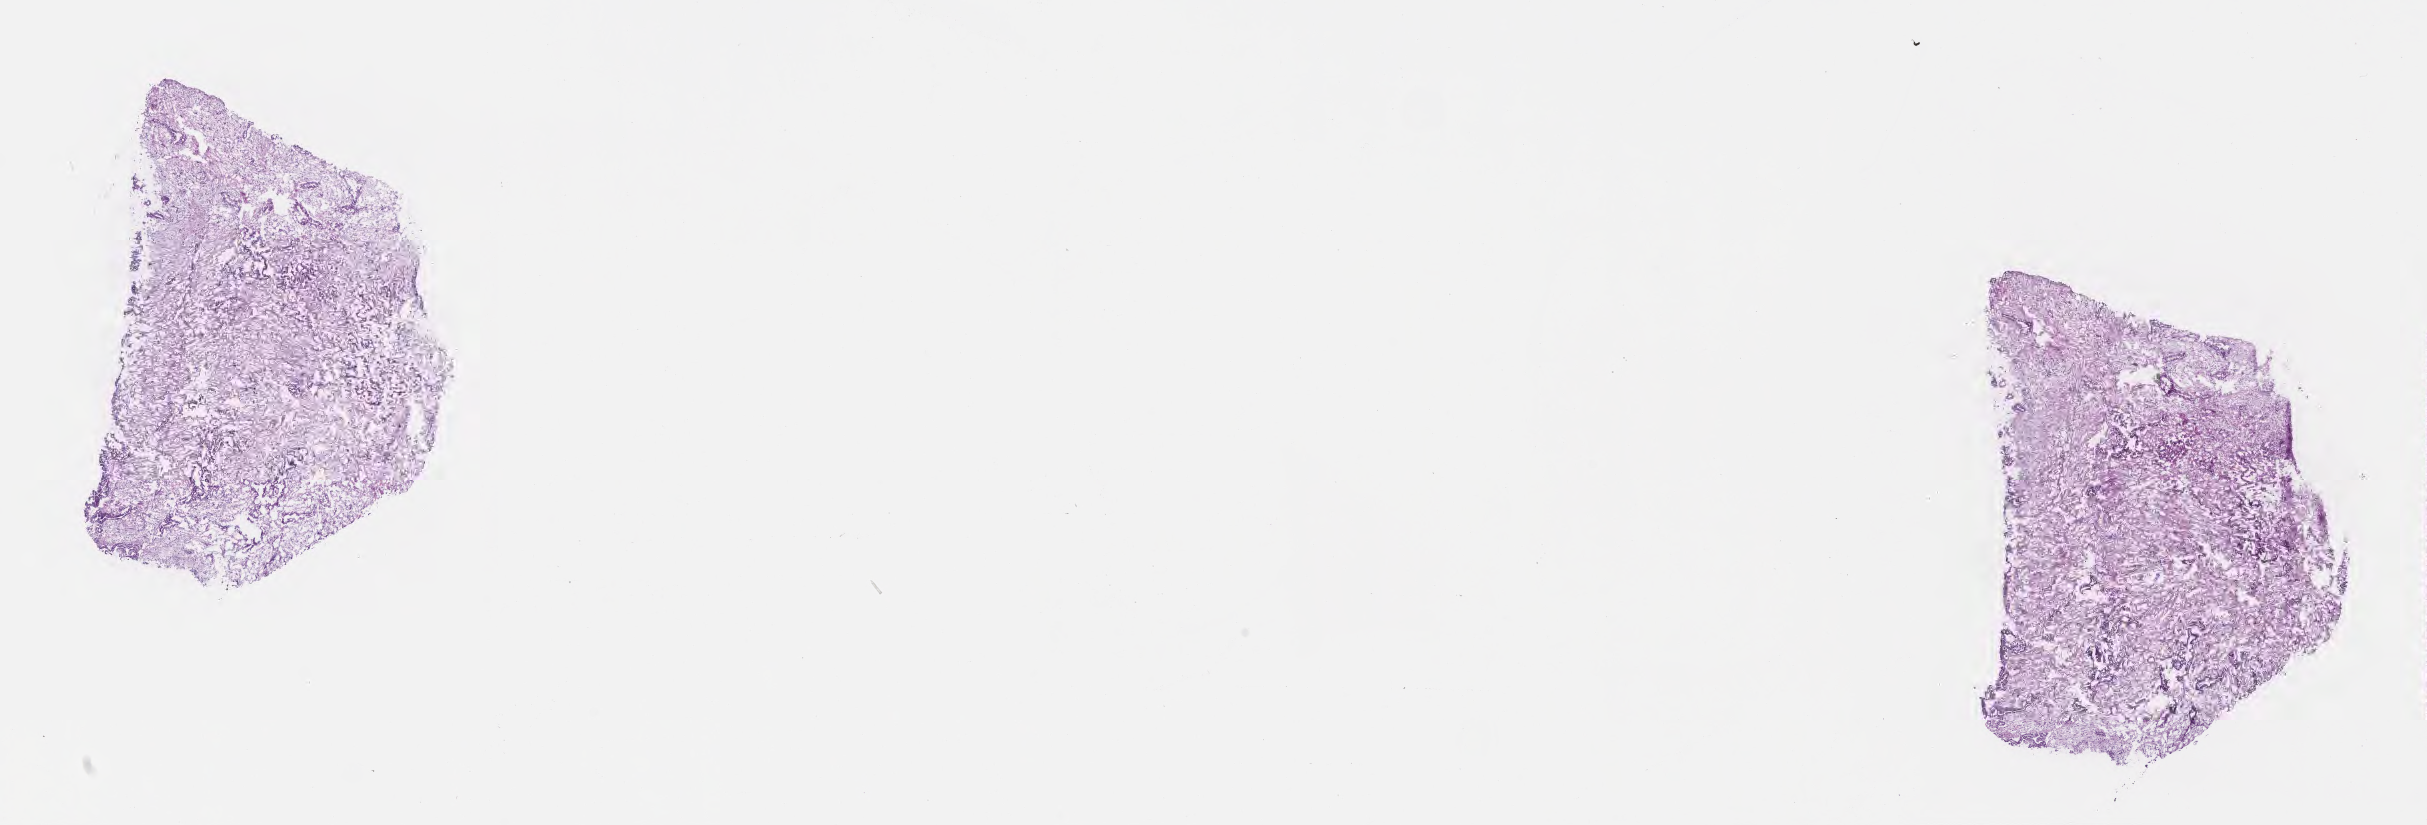
Digitized haematoxylin and eosin-stained section, low-resolution overview of the scanned area, about 19.6 x 6.7 mm, frozen section, primary tumor, site: body of pancreas. Male, age 72 years at initial diagnosis. Slide review estimates, as recorded: tumor cells 100%, tumor nuclei 15%, stromal cells 0%, necrosis 0%, normal cells 0%. Inflammatory infiltration, as recorded: lymphocyte infiltration 0%, monocyte infiltration 0%, neutrophil infiltration 0%.
* AJCC pathologic stage: Stage IIB
* section: top of the tissue portion
* histologic diagnosis: Adenocarcinoma, NOS